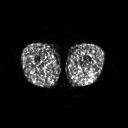
FDG PET of an extremity soft-tissue mass (from a PET/CT study), one axial slice; position 212 of 267 along the scan axis; 128 × 128 image matrix. Male patient, age 27 years. Case-level facts recorded for this patient, not image findings: histological type: extraskeletal osteosarcoma; grade: high; site of the primary tumour: left adductur.
Structures marked on this image (expert contour drawn on MRI and transferred to this co-registered scan by the dataset authors):
- gross tumour volume (mass): bounding box (x1, y1, x2, y2) in pixels: (82, 63, 87, 67)